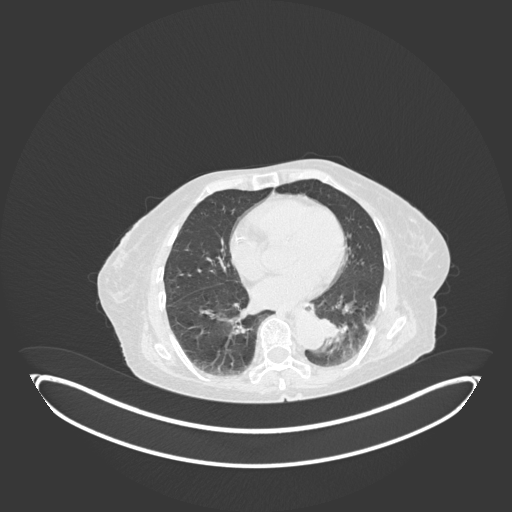
Chest CT, one axial slice; position 40 of 189 along the scan axis; 120 kVp; lung window (W 1500 / L -600 HU); 512 × 512 image matrix. Patient: female, 82 years. Case-level facts recorded for this patient, not image findings: clinical TNM (as recorded): T1b N0 M1.
Structures marked on this image (bounding box drawn by a radiologist):
- lung tumour (recorded histology: adenocarcinoma): bounding box (x1, y1, x2, y2) in pixels: (319, 313, 351, 348)